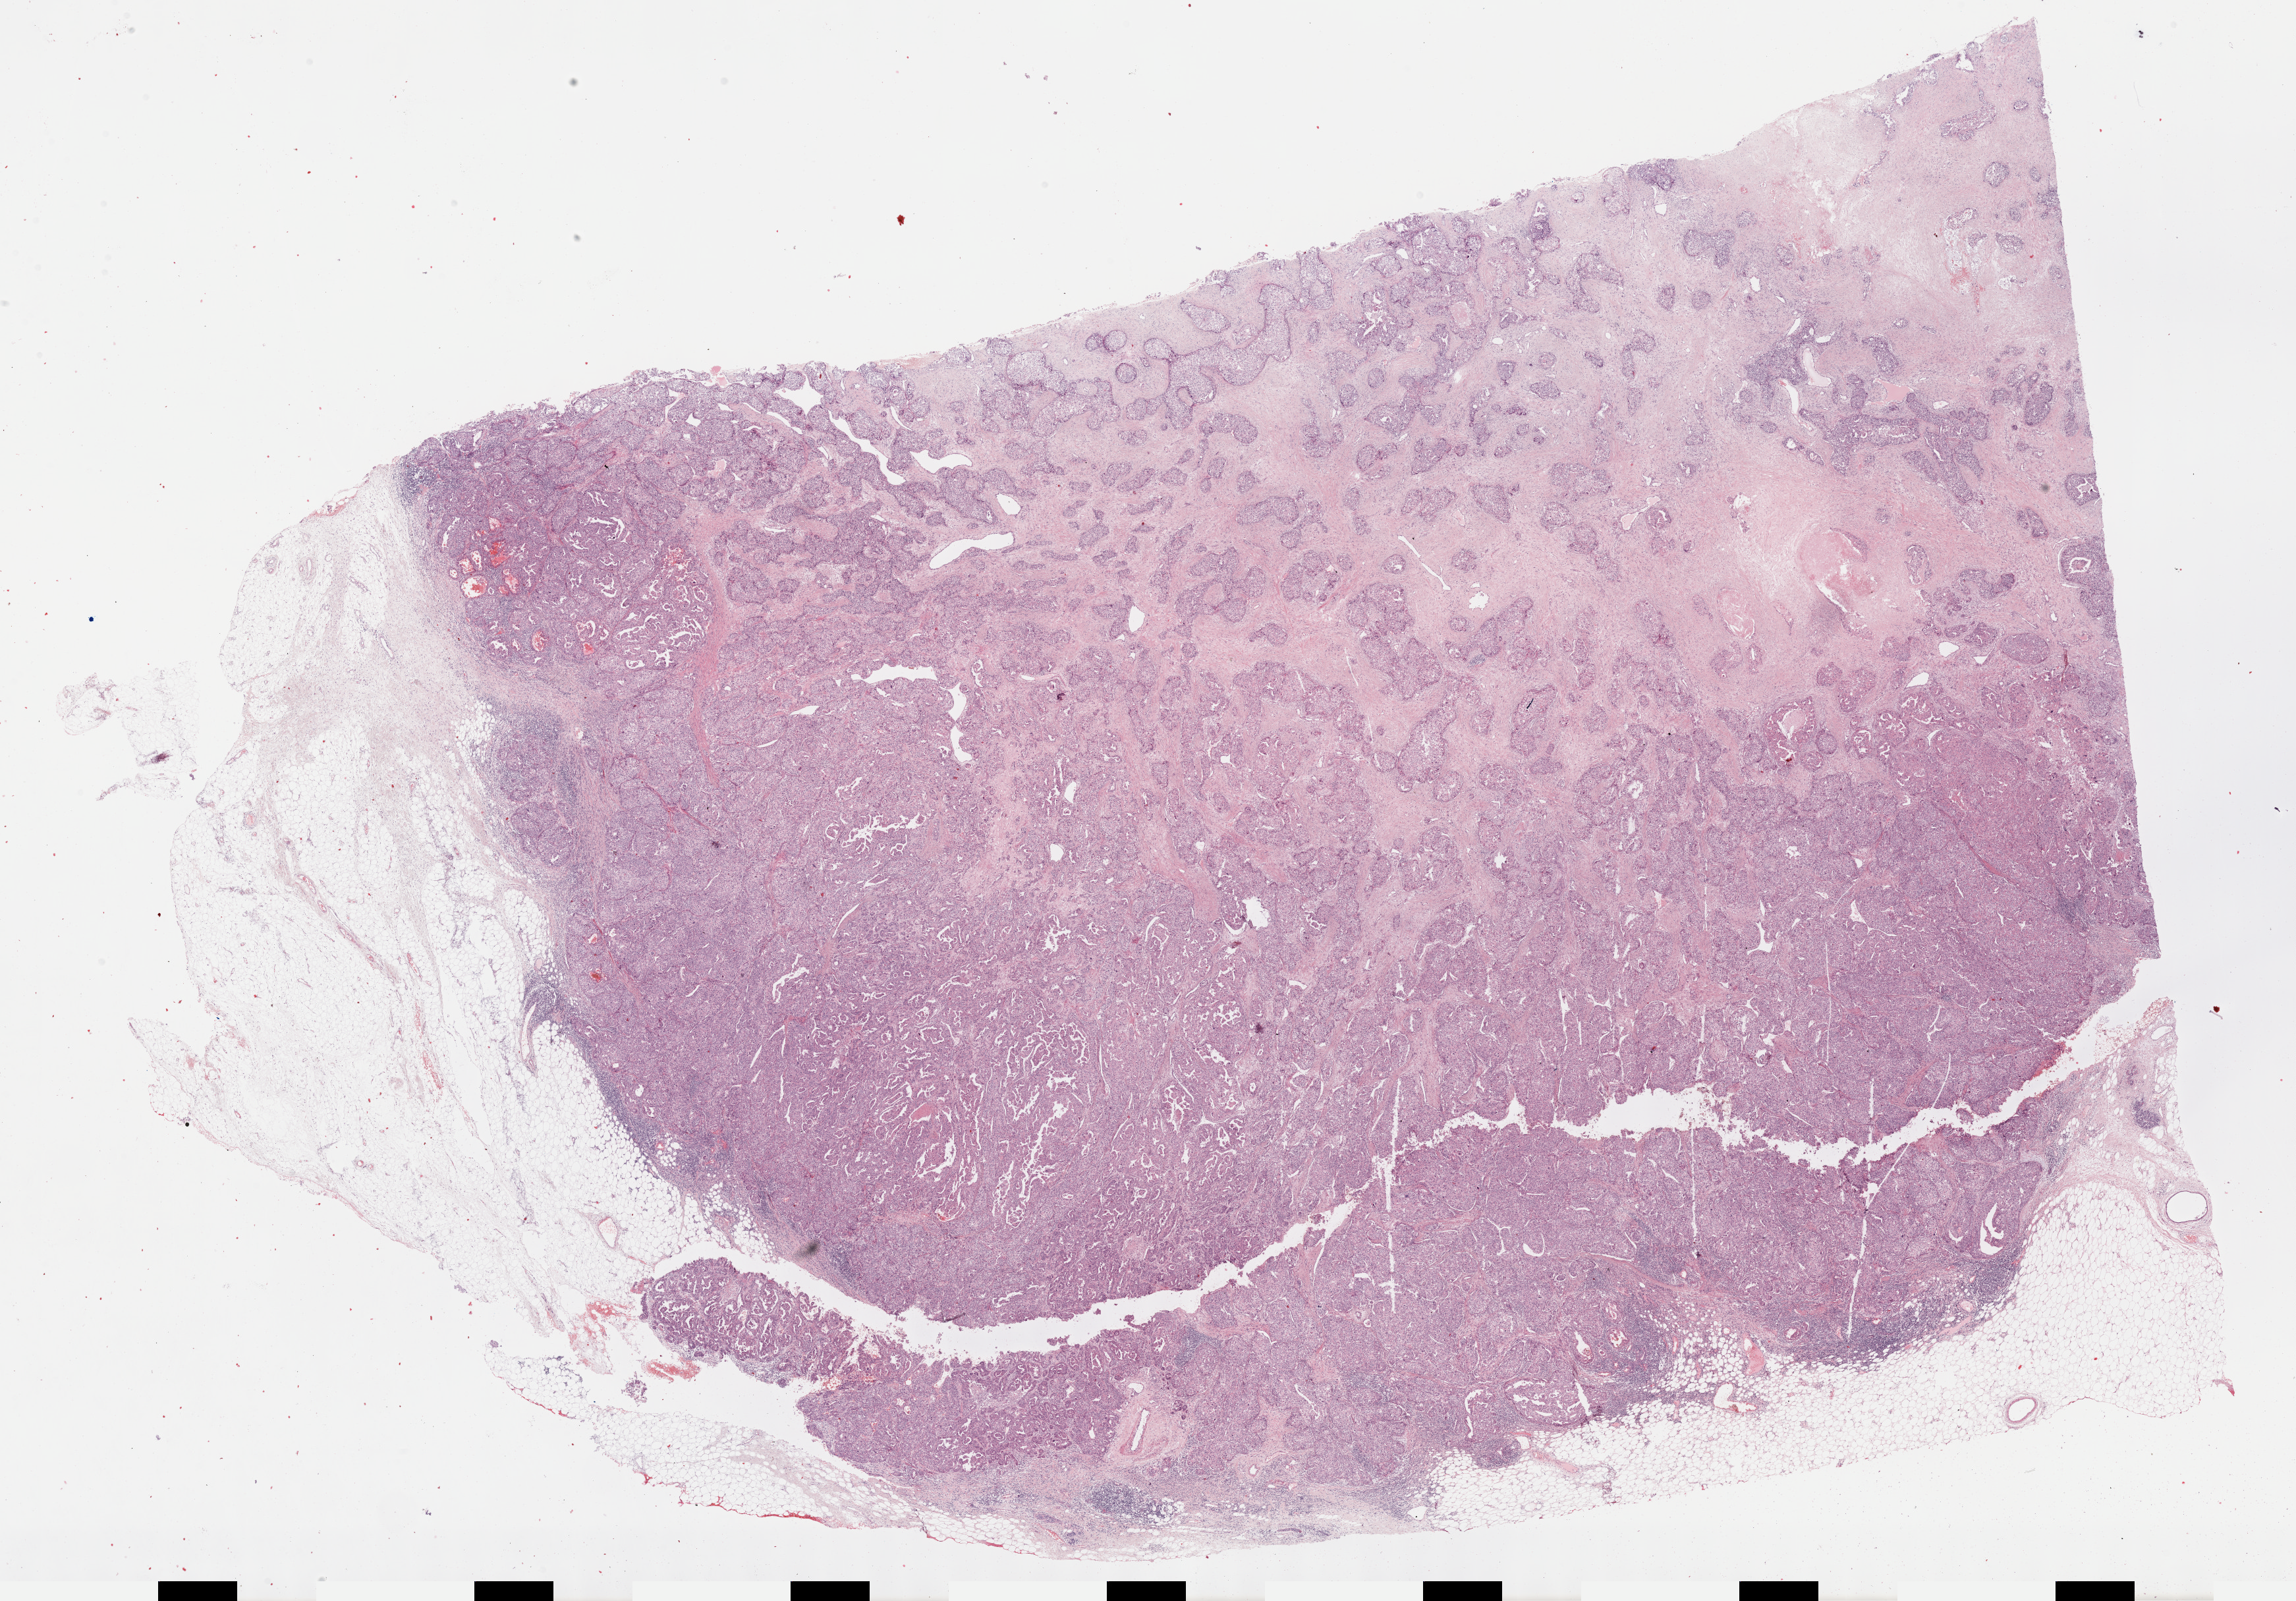
Whole-slide histology image, Hematoxylin and eosin (H&E) stained, whole scanned area (about 28.2 x 19.7 mm) shown as a low-resolution overview, FFPE section, breast, primary tumour sample. Female patient; age at initial diagnosis 53 years.
AJCC pathologic stage: IIA (7th edition). Diagnosis: Infiltrating duct carcinoma, NOS. Laterality: left.